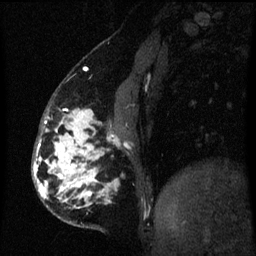
Breast MRI (dynamic contrast-enhanced), one sagittal slice; slice 20 of 60 in the series (ordered by position); dynamic contrast-enhanced series, image 2 of 3 at this slice position (ordered by acquisition); 1.5 T; TE 4.2 ms, TR 8 ms; 256 × 256 image matrix, field of view 190 × 190 mm. Female patient, age 50 years.
Outlined on this slice (semi-automatically segmented with operator editing):
- analysis volume of interest (the breast-tissue region the enhancement analysis was run in; not a lesion): bounding box (x1, y1, x2, y2) in pixels: (32, 109, 119, 226)
- tumour enhancement mask (voxels above the 70 % enhancement threshold inside the analysis volume of interest): (34, 110, 116, 208)